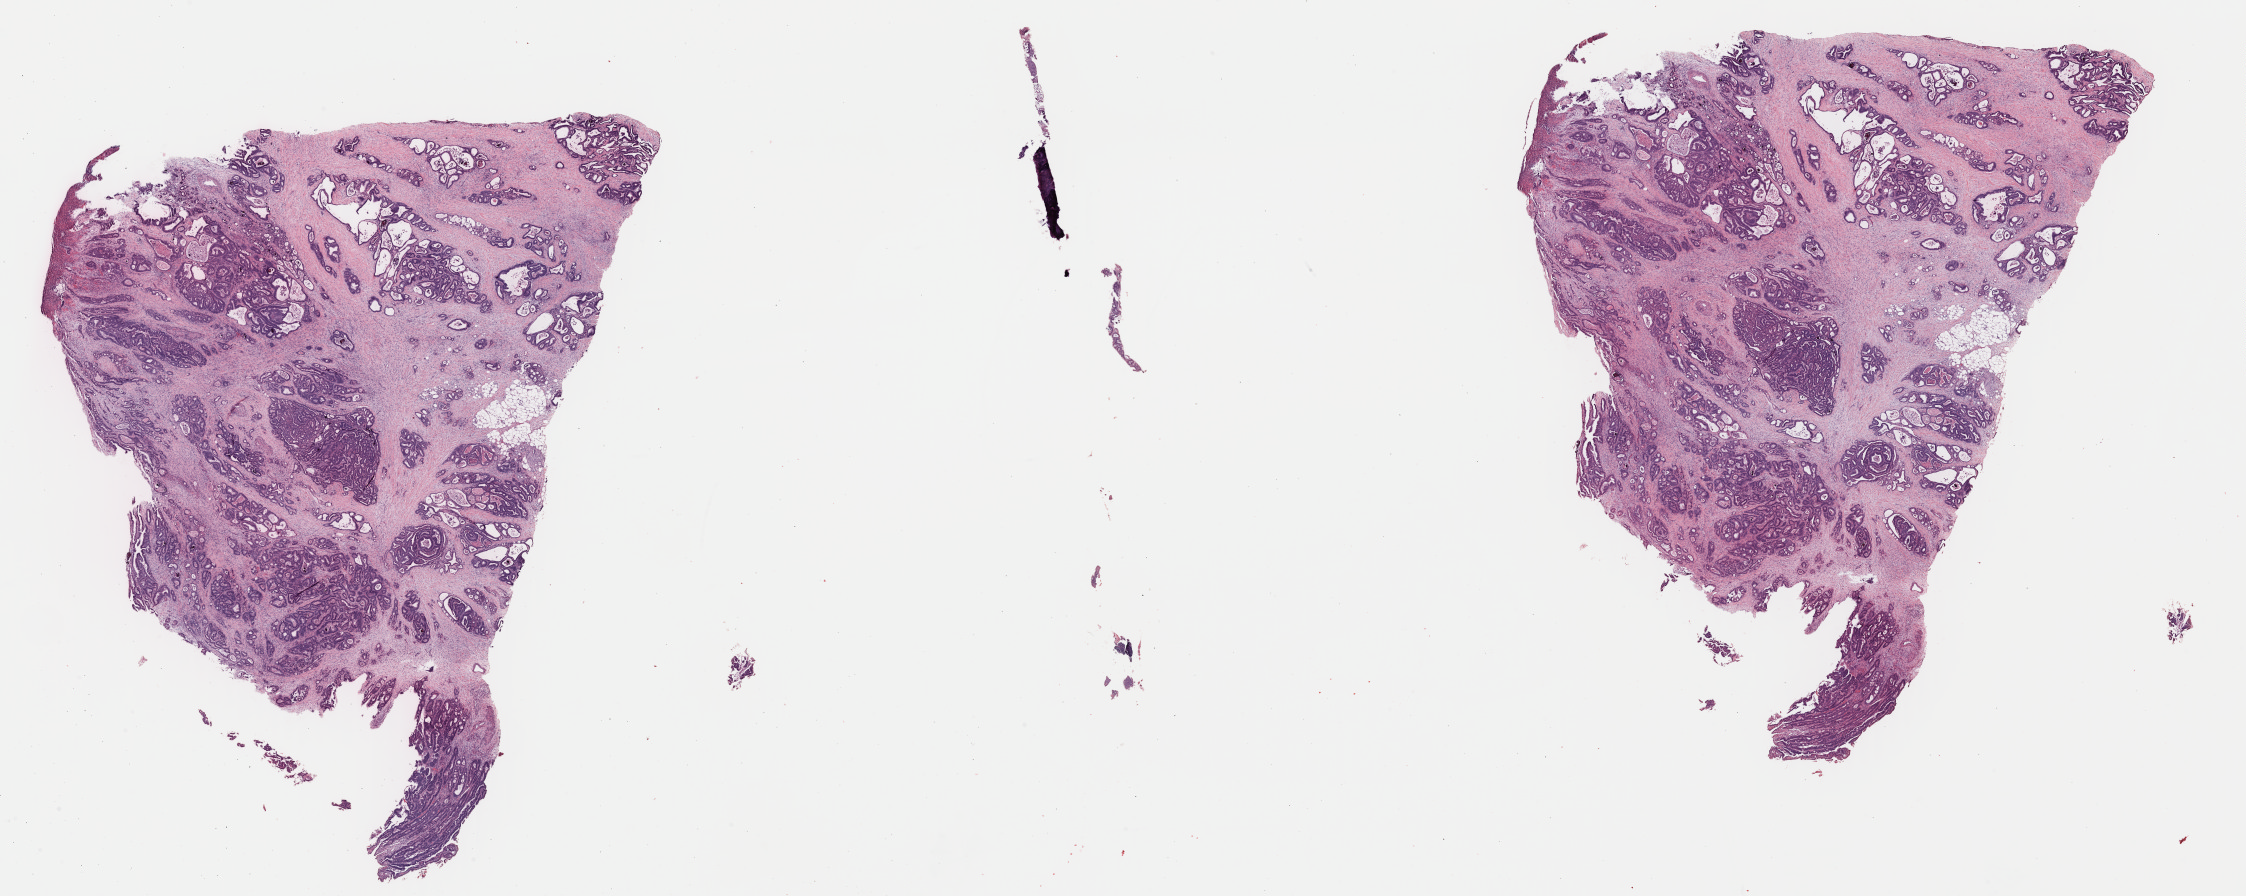
Hematoxylin and eosin (H&E) stained whole-slide image, shown as a low-resolution overview of the whole scanned area (about 35.4 x 14.1 mm, acquisition: 40x scan), formalin-fixed paraffin-embedded (FFPE) diagnostic section, colon, primary tumour sample. Male, age 56 years at initial diagnosis.
Diagnosis: Adenocarcinoma, NOS (sigmoid colon). AJCC pathologic stage: IV (6th edition).